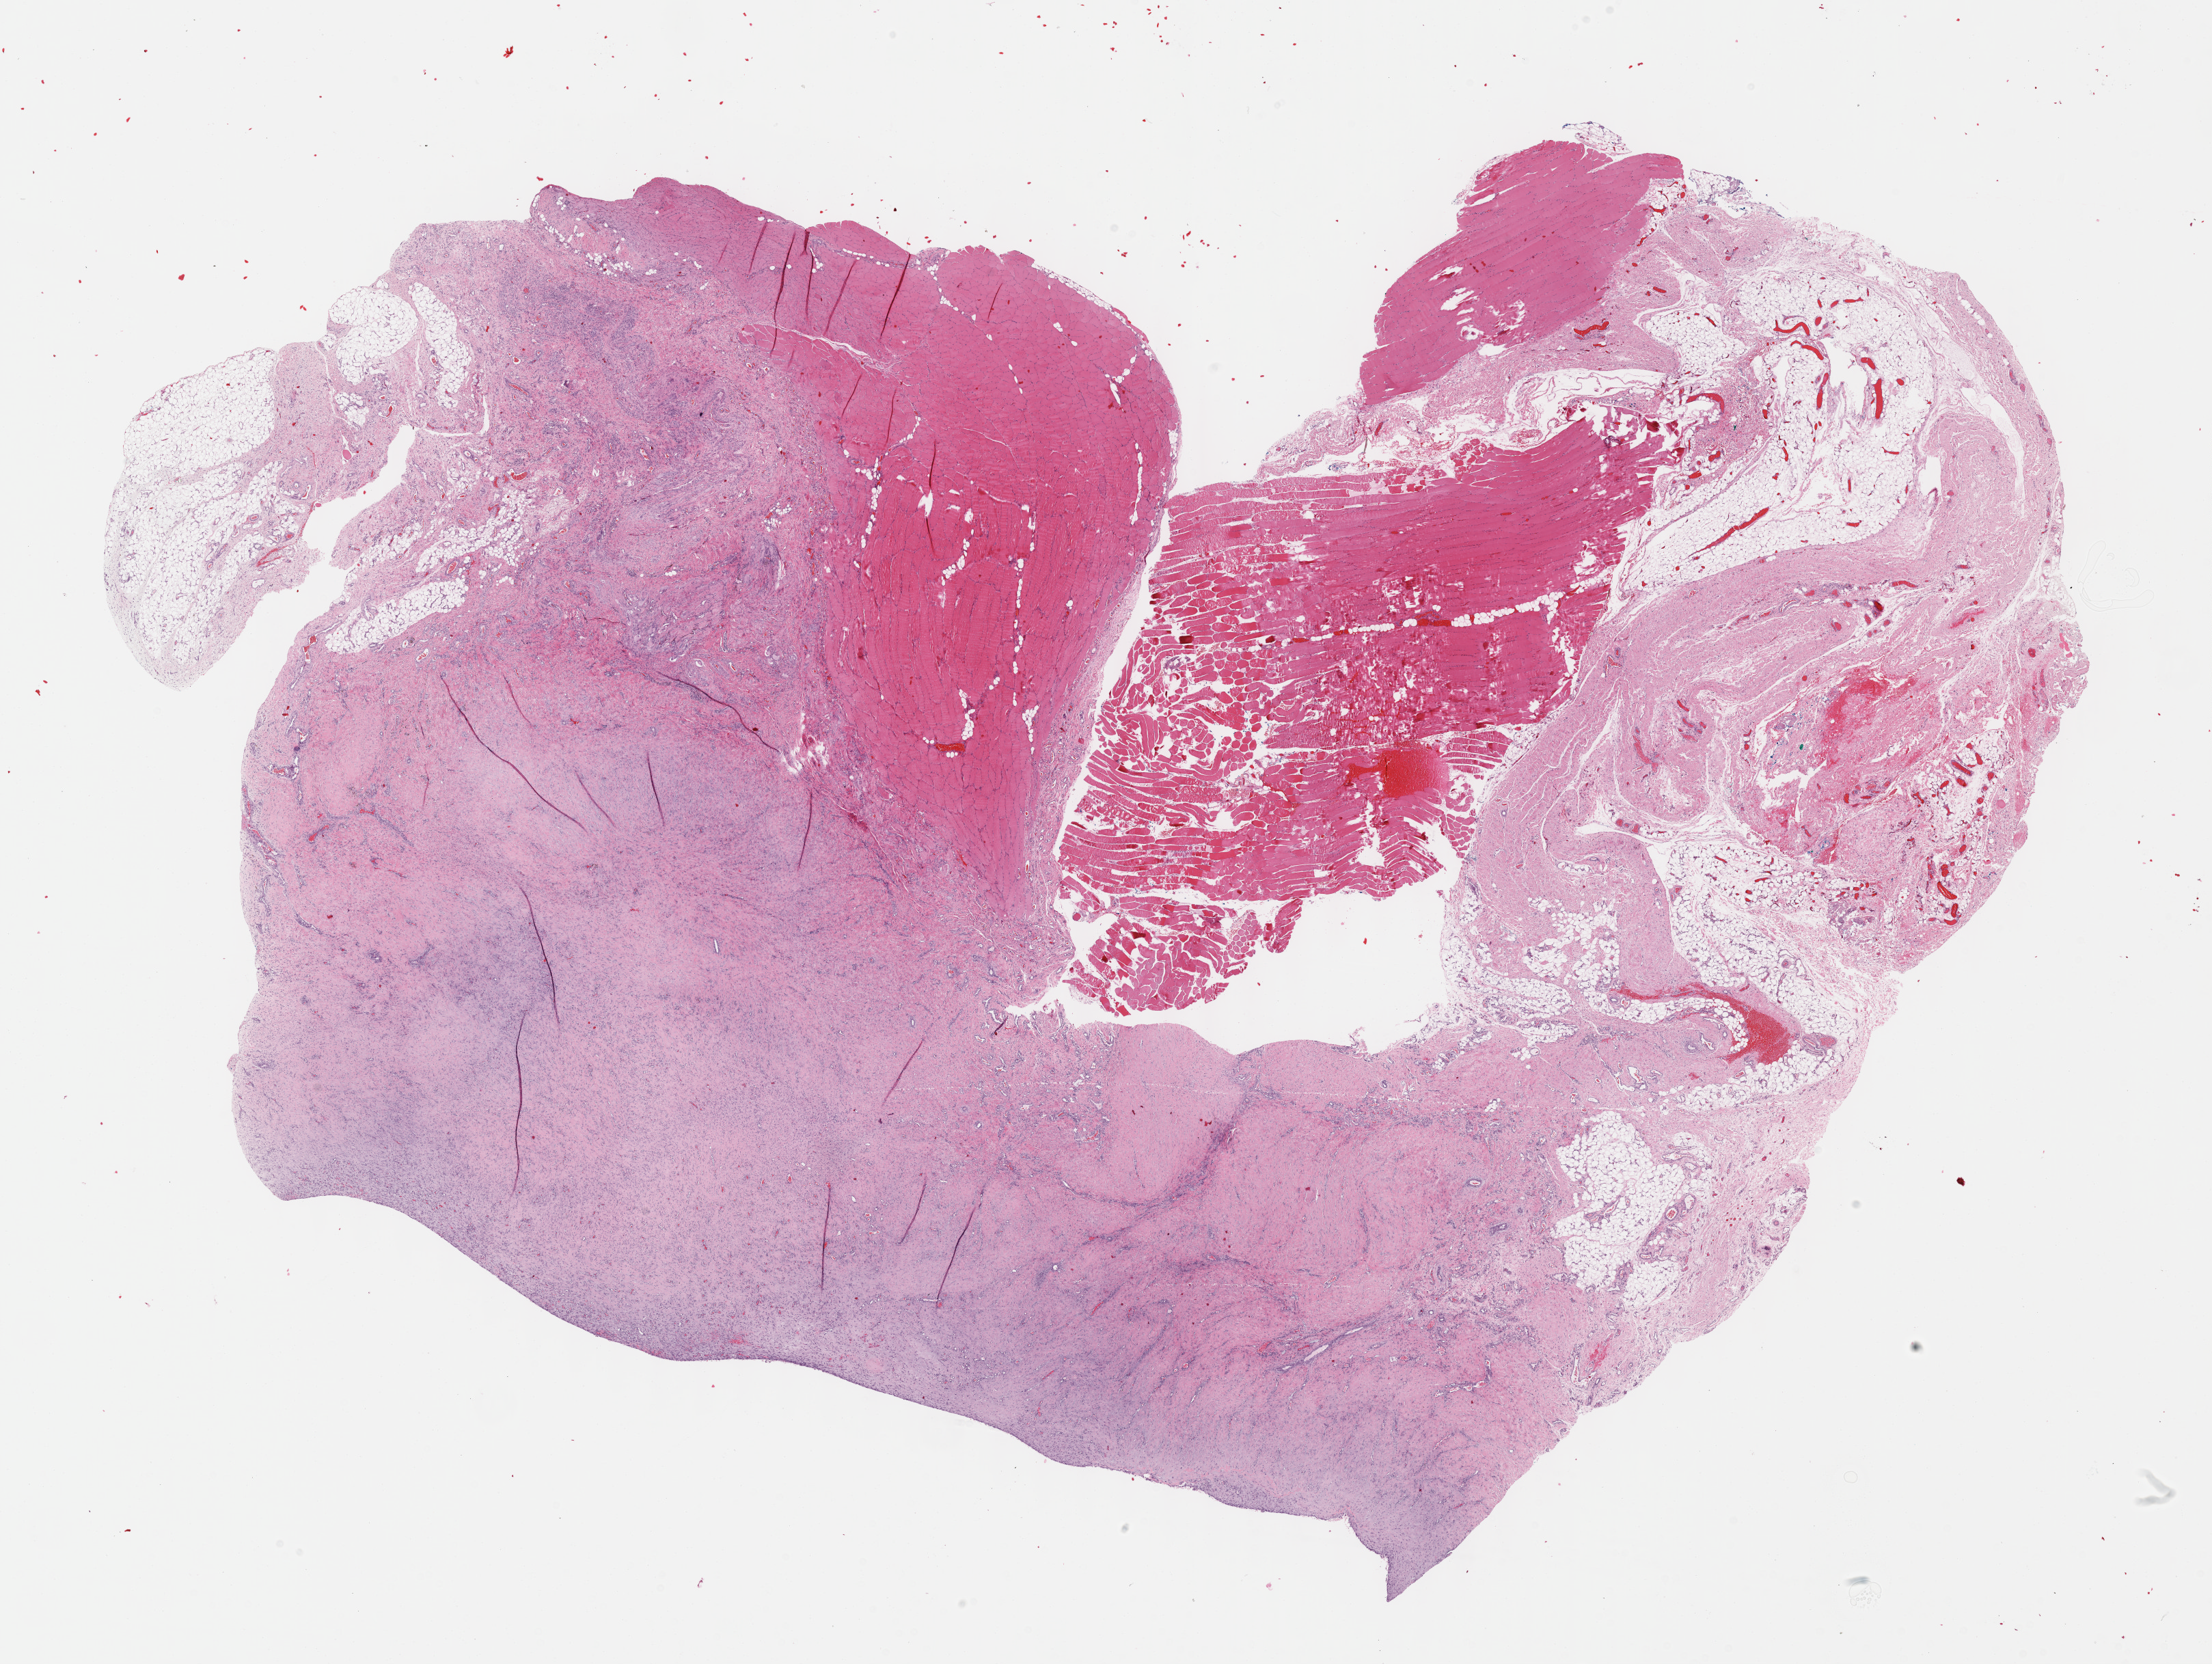
Digitized H&E-stained tissue section (whole slide), a low-resolution overview of the entire scanned area, about 26.2 x 19.7 mm (acquisition: 40x scan); formalin-fixed paraffin-embedded (FFPE) diagnostic section; primary tumour sample from the connective, subcutaneous and other soft tissues. Male patient; age at initial diagnosis 35 years.
* diagnosis: Fibromyxosarcoma (connective, subcutaneous and other soft tissues of lower limb and hip)